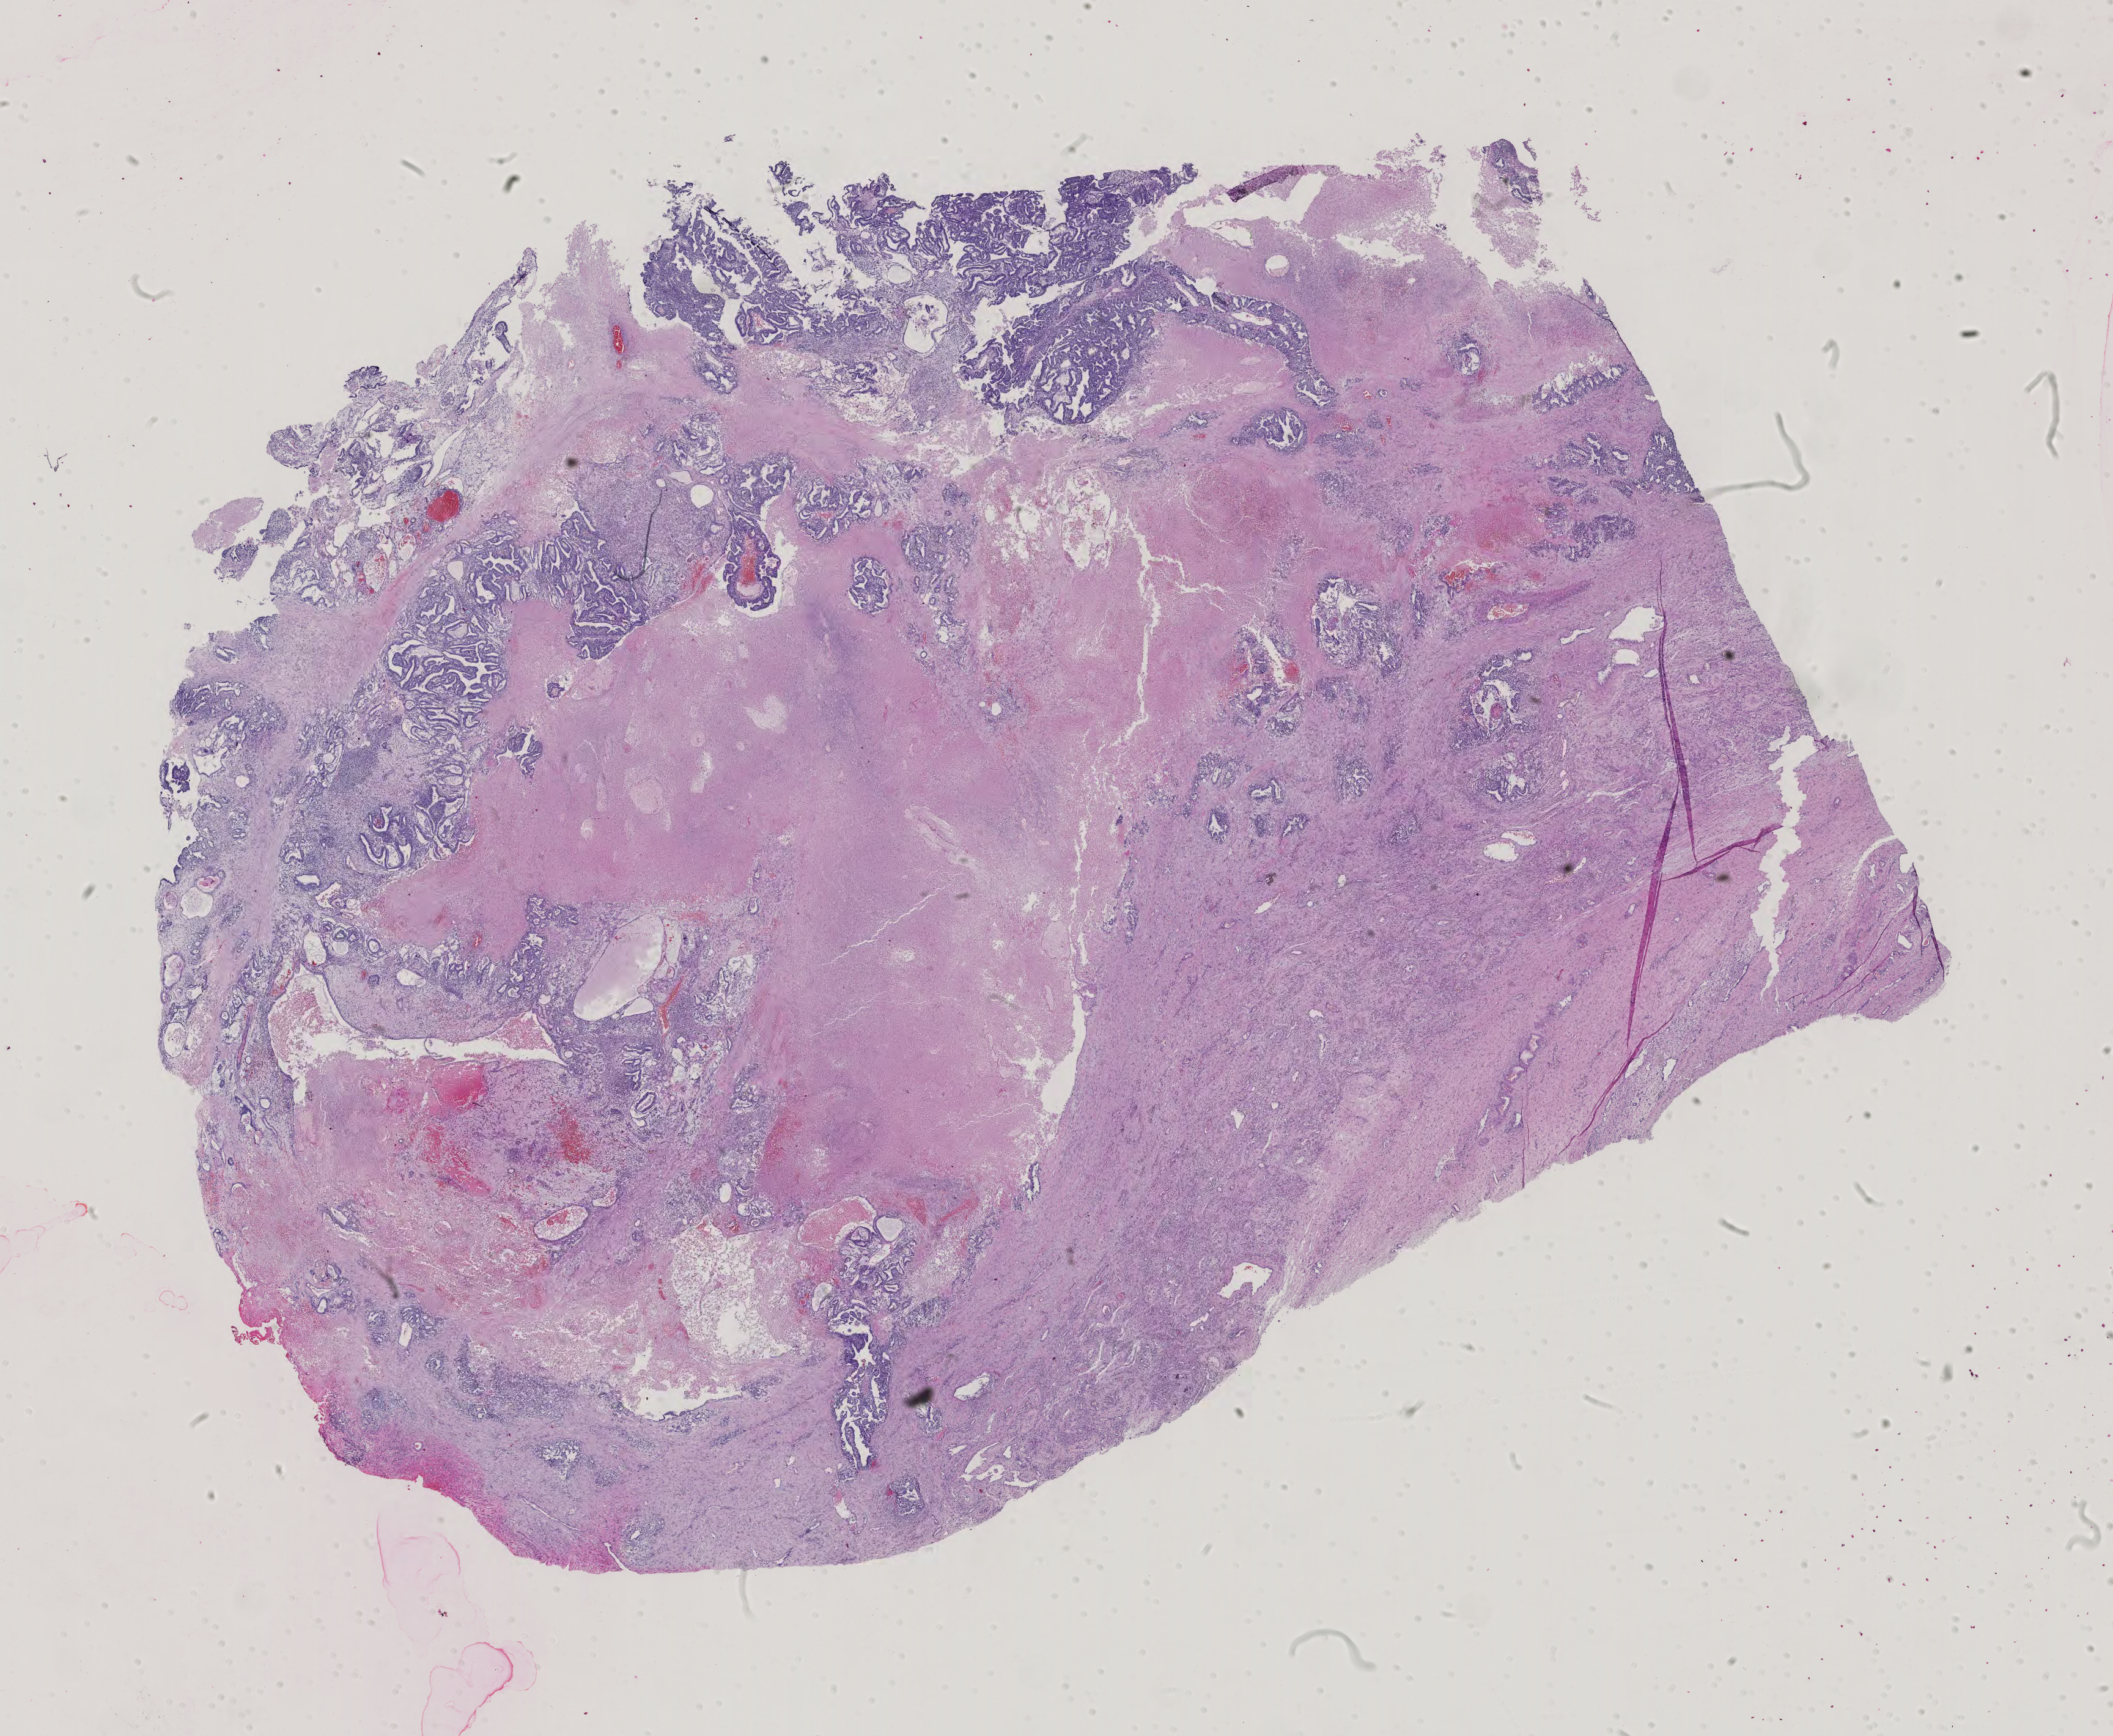
Whole-slide histology image, H&E-stained, whole scanned area (about 25.2 x 20.7 mm, from a 40x scan) shown as a low-resolution overview. FFPE section. Sample: primary tumour, testis. Patient: male, age at initial diagnosis 32 years.
Laterality: right. TNM: T3 NX M1. AJCC pathologic stage: III. Histologic diagnosis: Mixed germ cell tumor.